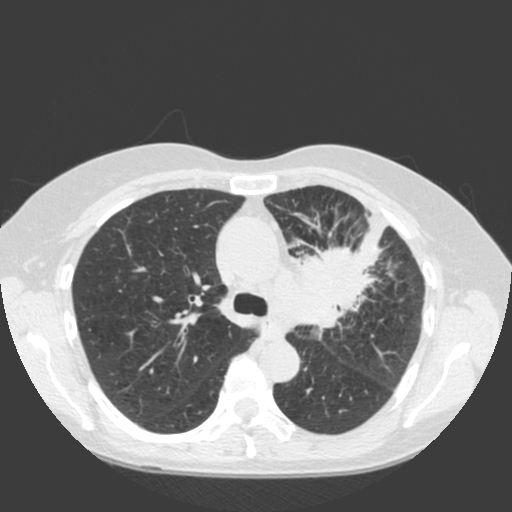
Chest CT (low-dose screening protocol), one axial image. First (baseline) screen. Lung window (W 1500 / L -600 HU). Standard (soft-tissue) reconstruction kernel (C). Slice 56 of 184 in the series. 512 × 512 image matrix. Female, age 66 years at enrolment. Current smoker at enrolment.
Expert-annotated lung lesion, box from (x=283, y=228) to (x=399, y=332) px. The exam's reader record, not a measurement of the box and not confirmed to be the same lesion: non-calcified nodule or mass ≥4 mm, left upper lobe, 61 × 45 mm, spiculated (stellate) margins, soft tissue attenuation. Official screen result: positive, change unspecified: nodule(s) >= 4 mm or enlarging nodule(s), mass(es), or other non-specific abnormalities suspicious for lung cancer. Later outcome: lung cancer diagnosed 19 days after this screen — squamous cell carcinoma, keratinizing, NOS, left upper lobe, left hilum, mediastinum, left main stem bronchus, other location, poorly differentiated (G3), stage IIIB (AJCC 6th edition), 60 mm at pathology.